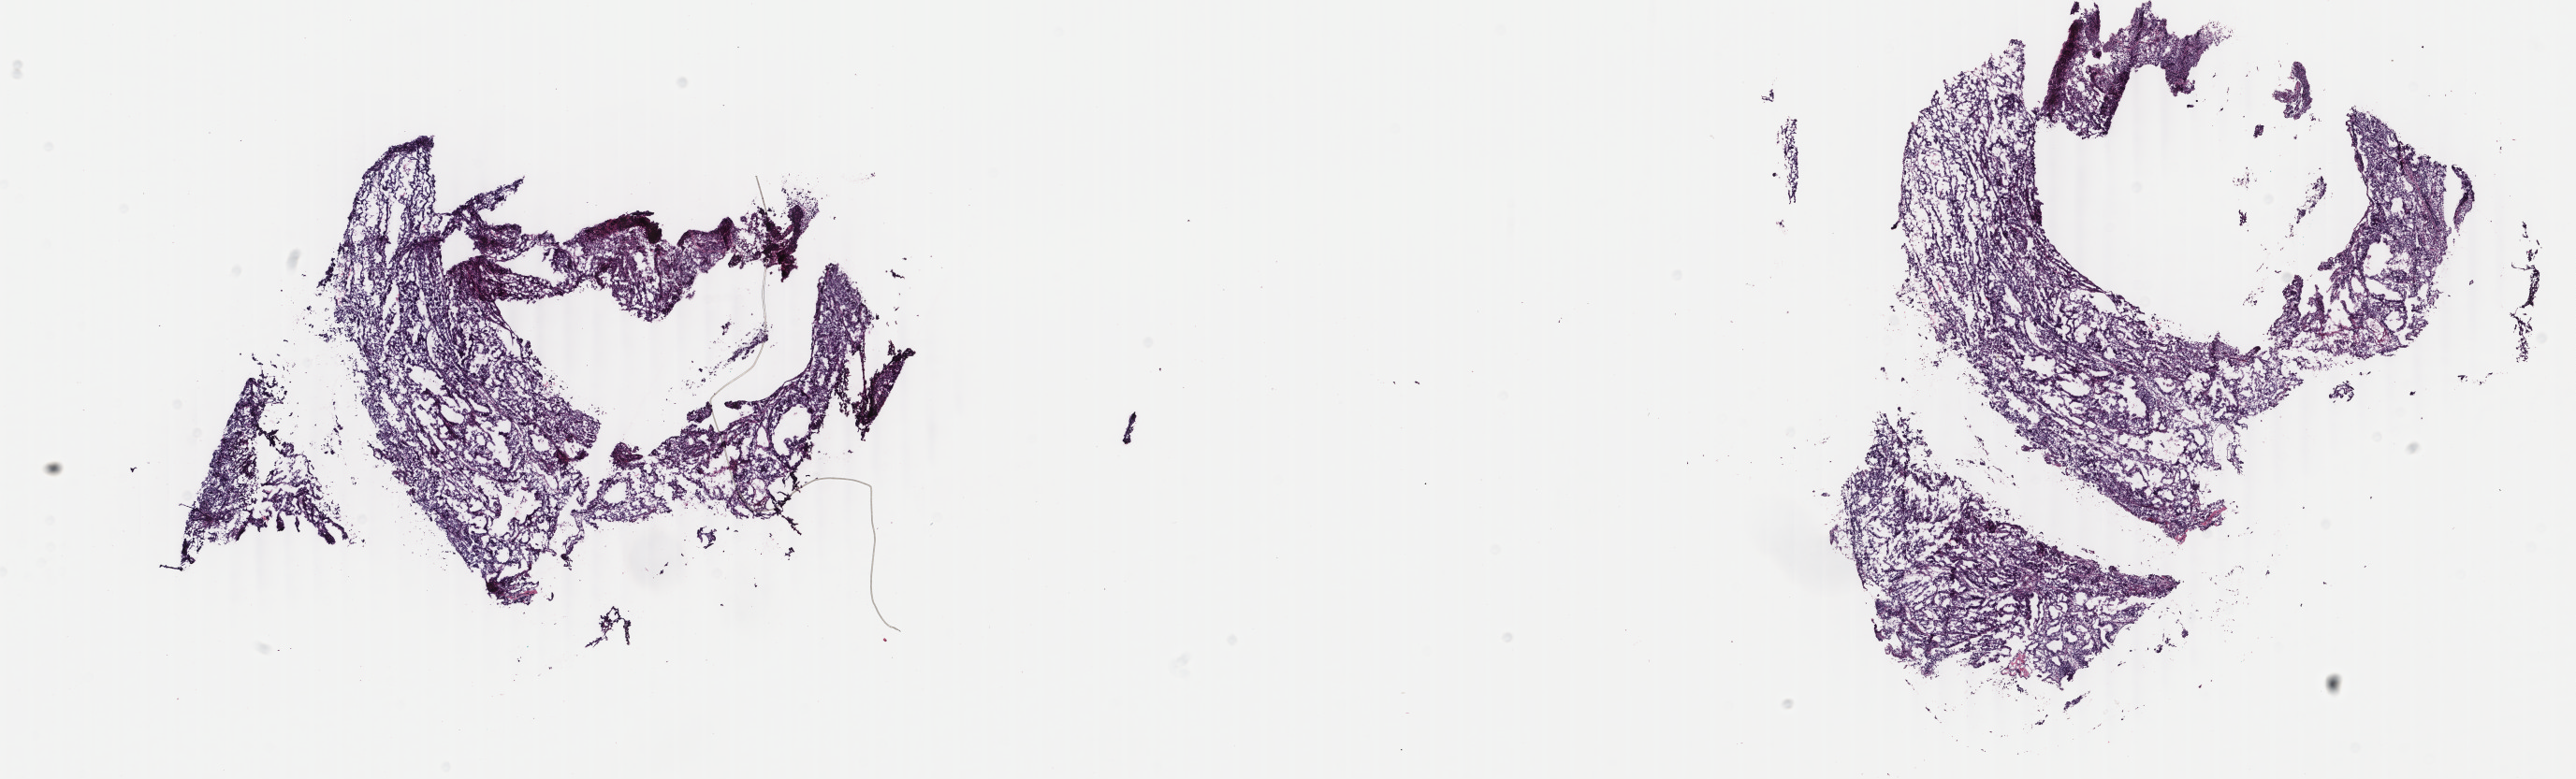
Digitized H&E-stained tissue section (whole slide) — low-resolution overview of the scanned area, about 21.9 x 6.6 mm; frozen section from the bottom of the tissue portion; uterus, primary tumour sample. Female, age 76 years at initial diagnosis. Histologic grade: G1 (well differentiated). Composition of this section per pathologist review: tumour cells 70%, tumour nuclei 70%, normal cells 0%, stromal cells 30%, necrosis 0%. Inflammatory infiltration, as recorded: lymphocyte infiltration 30%, monocyte infiltration 40%, neutrophil infiltration 20%.
• FIGO stage: IA
• lymph nodes positive (case pathology): 0 of 10 examined
• diagnosis: Endometrioid adenocarcinoma, NOS